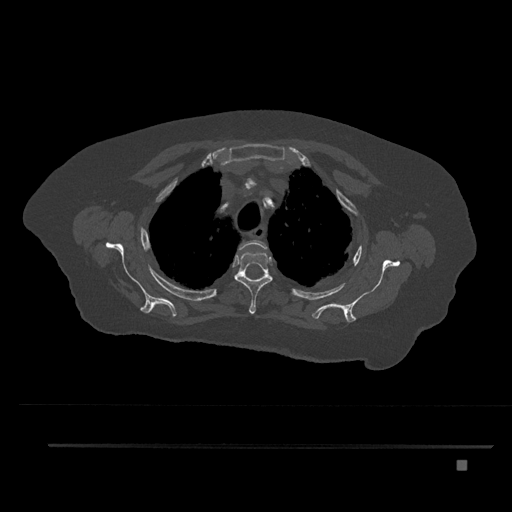
CT including the spine, one axial slice. Position 637 of 797 along the scan axis. Reconstruction kernel Br40s/3. 120 kVp. Bone window (W 1800 / L 400 HU). 0.5 mm slice thickness. 512 × 512 image matrix, field of view 437 × 437 mm. Patient: female, 76 years. Case-level facts recorded for this patient, not image findings: primary cancer: lung; vertebrae with lytic lesions (as recorded): T11, L3.
Structures marked on this image (semi-automatically segmented with operator editing):
- T2 vertebra: box from (x=237, y=240) to (x=267, y=255) px
- T3 vertebra: (x=234, y=253)–(x=273, y=314)